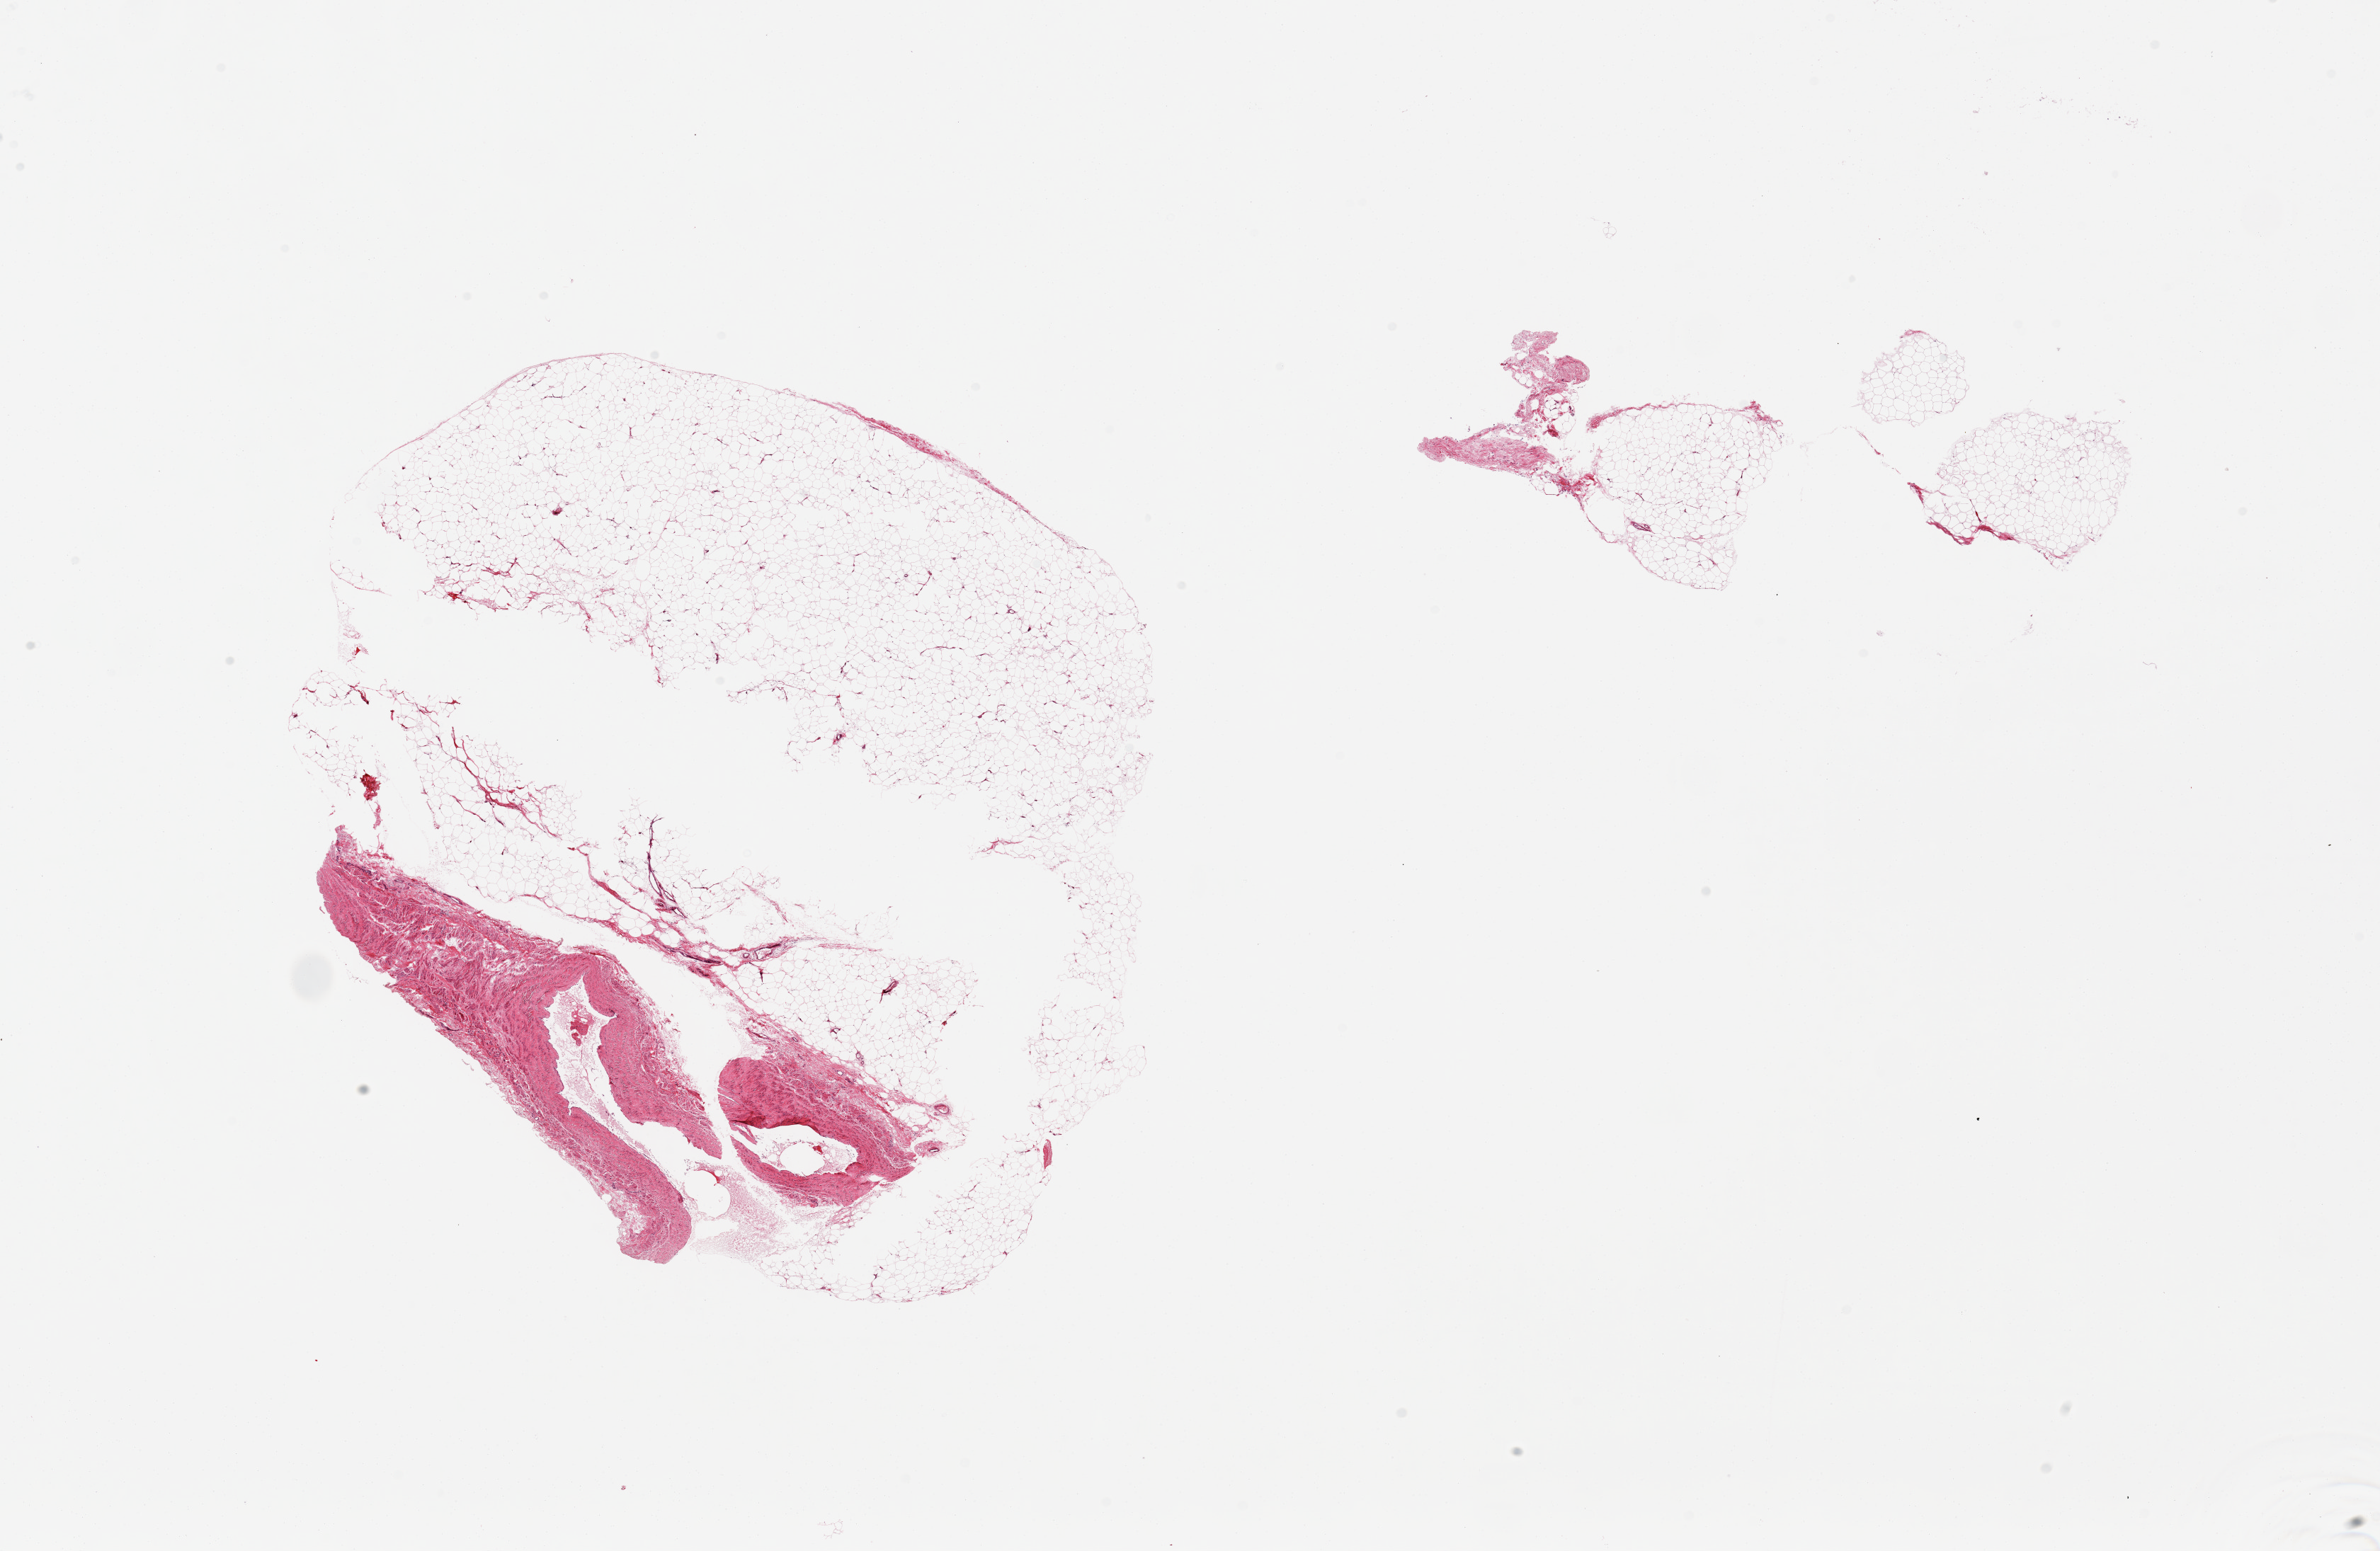
Whole-slide image, H&E stain — whole scanned area (about 26.6 x 17.3 mm, from a 20x scan) shown as a low-resolution overview, PAXgene-fixed, paraffin-embedded tissue, target tissue: adipose tissue, donor tissue sample. Donor sex: male.
• reviewer comment on this tissue sample: 2 pieces; large blood vessel along one edge